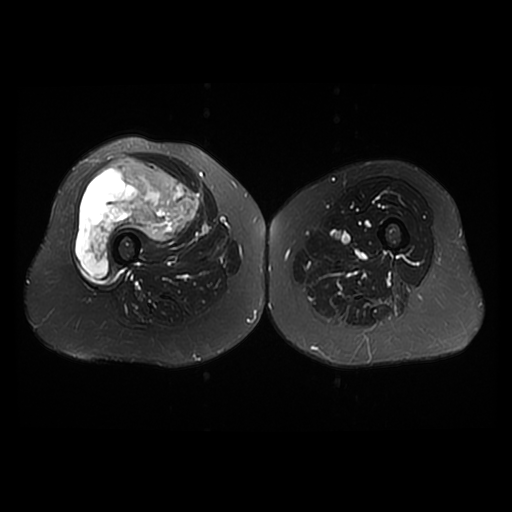
MRI of an extremity soft-tissue mass, one axial slice. Slice 21 of 42 in the series (ordered by position). T2-weighted fat-saturated. 6 mm slice thickness. 512 × 512 image matrix, field of view 440 × 440 mm. Female patient. From the clinical record (not read from this slice): histological type: pleiomorphic undifferentiated sarcoma; grade: high; site of the primary tumour: right quadricep.
Outlined on this slice (outlined manually by an expert reader):
- gross tumour volume including surrounding oedema: box from (x=74, y=158) to (x=199, y=279) px
- gross tumour volume (mass): (x=74, y=158)–(x=199, y=279)